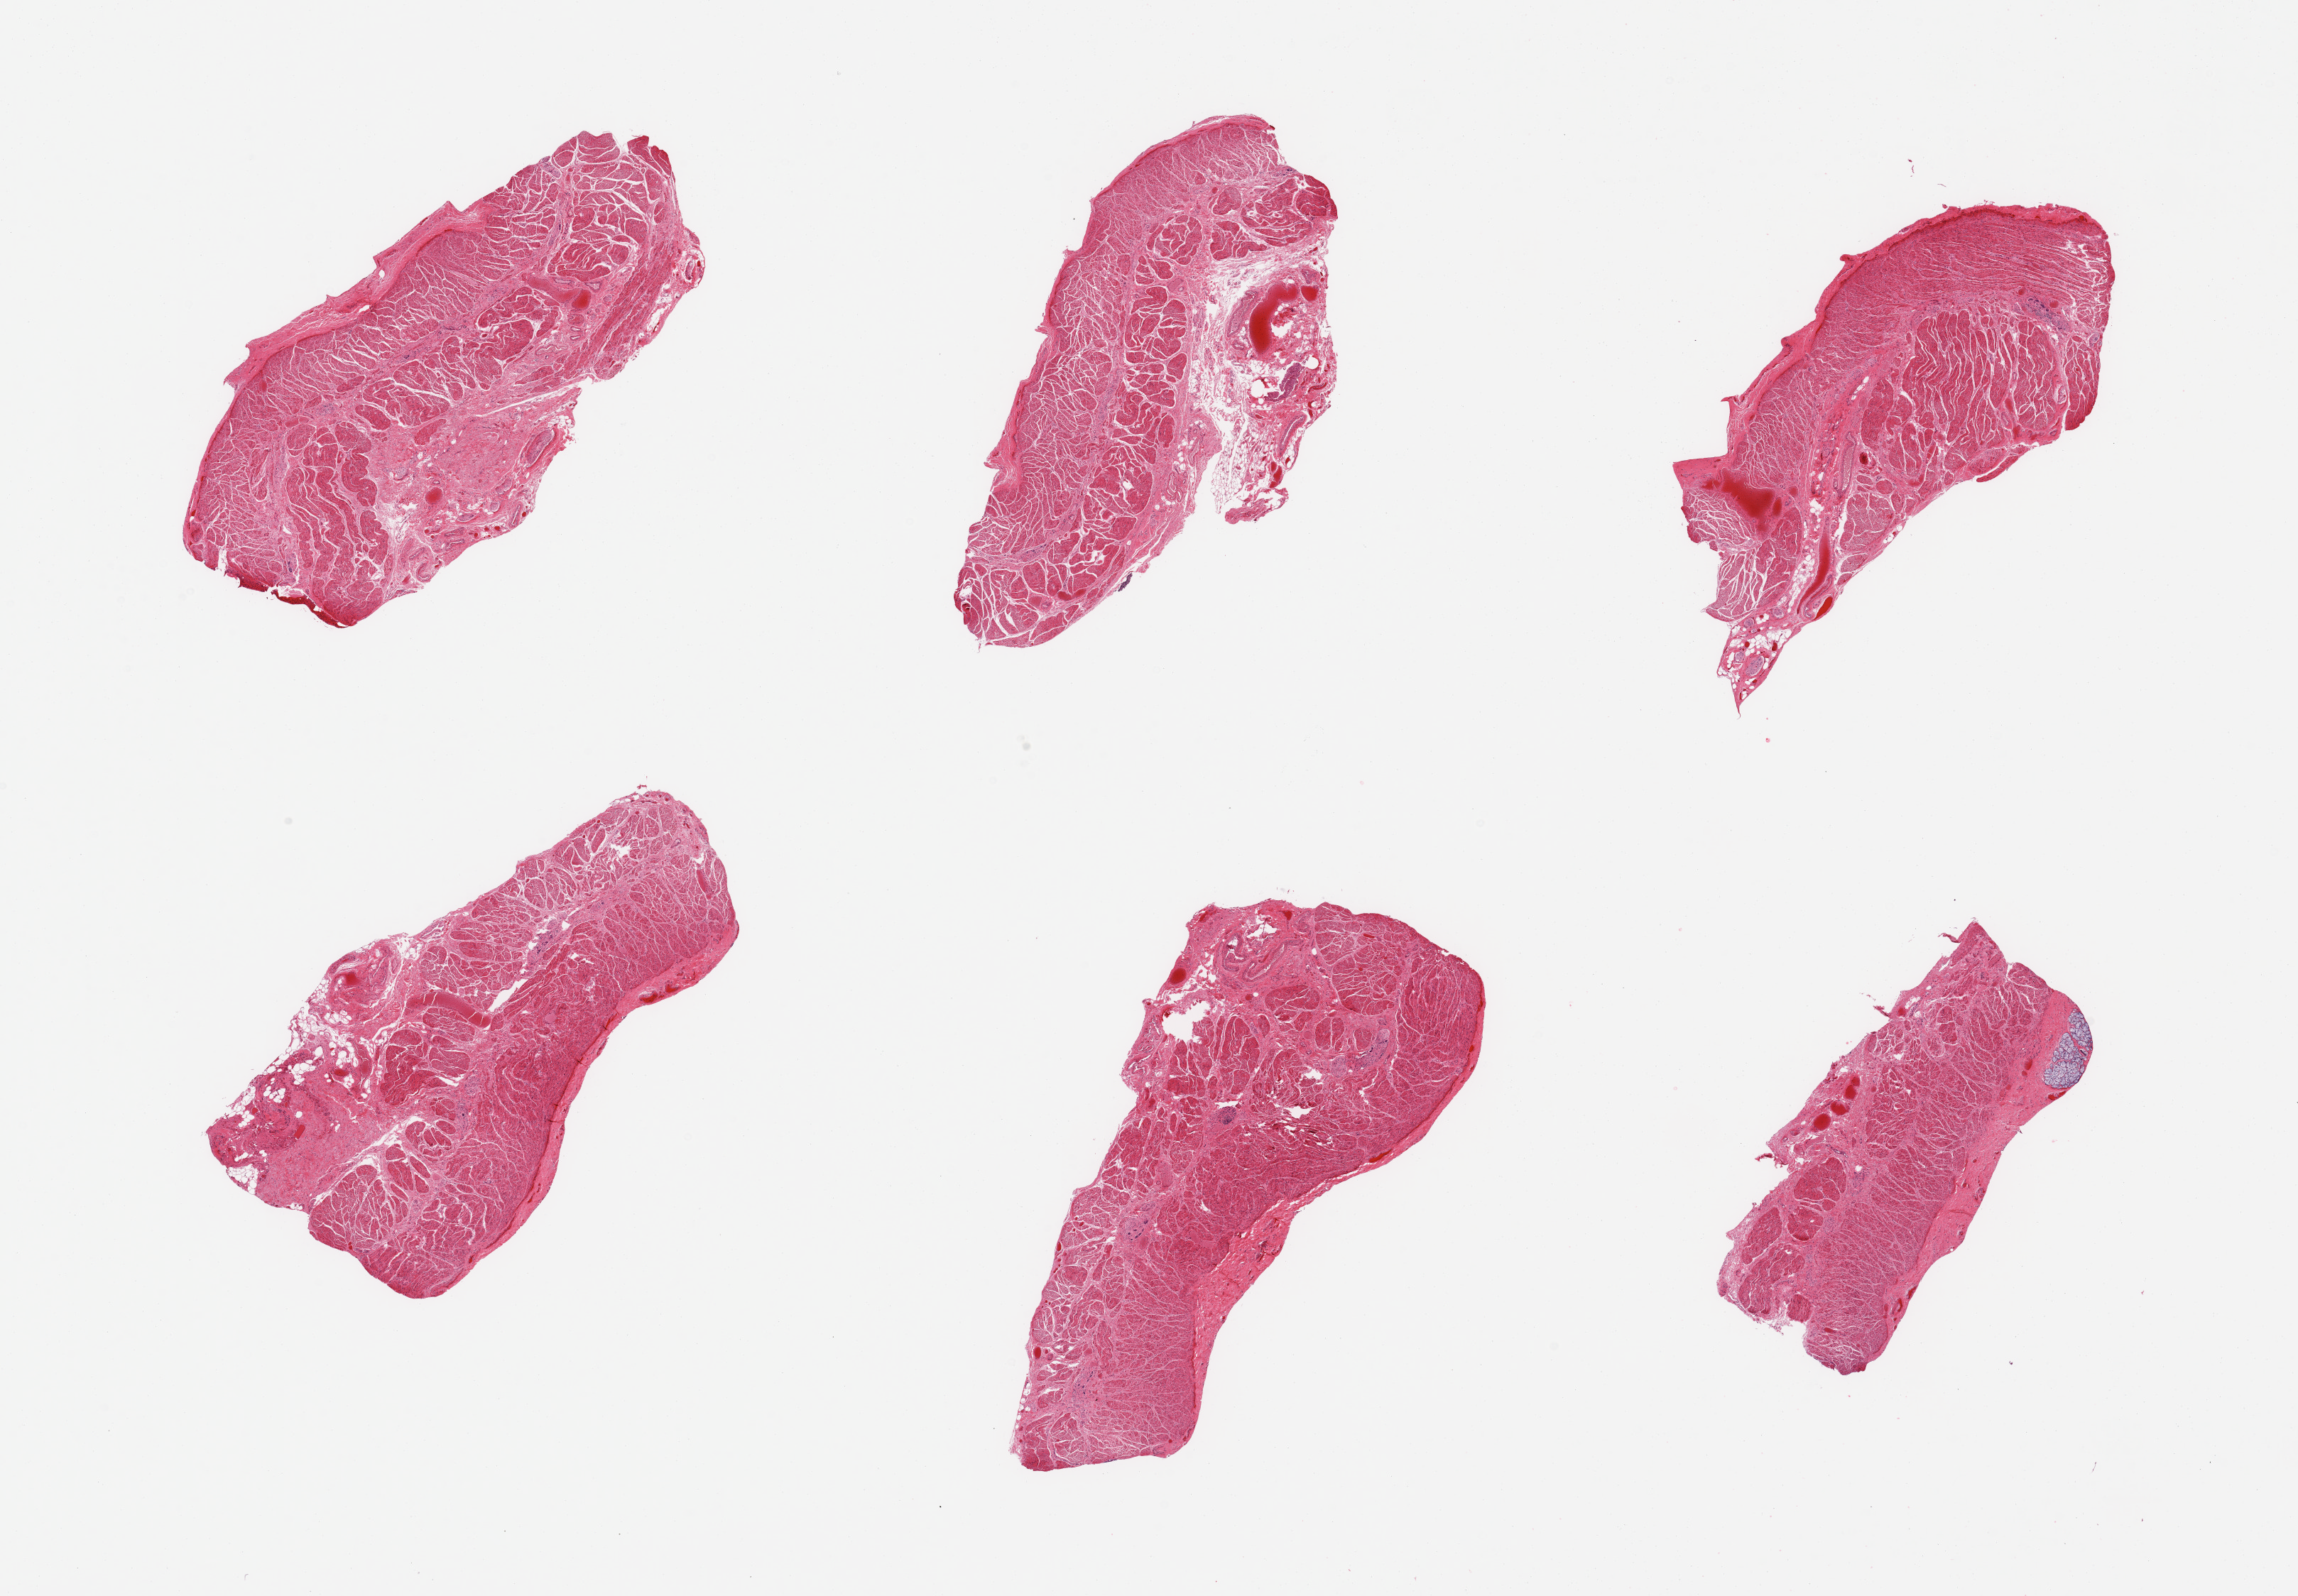
H&E whole-slide image, shown as a low-resolution overview of the whole scanned area (about 25.6 x 17.8 mm); PAXgene-fixed paraffin-embedded (PFPE) section; section of esophageal muscle (target tissue); donor tissue sample. Donor sex: male.
Pathologist's review note for this sample: 6 pieces; mostly target muscularis with small portions of residual attached fat/vessels/nerve/submucosal glands.